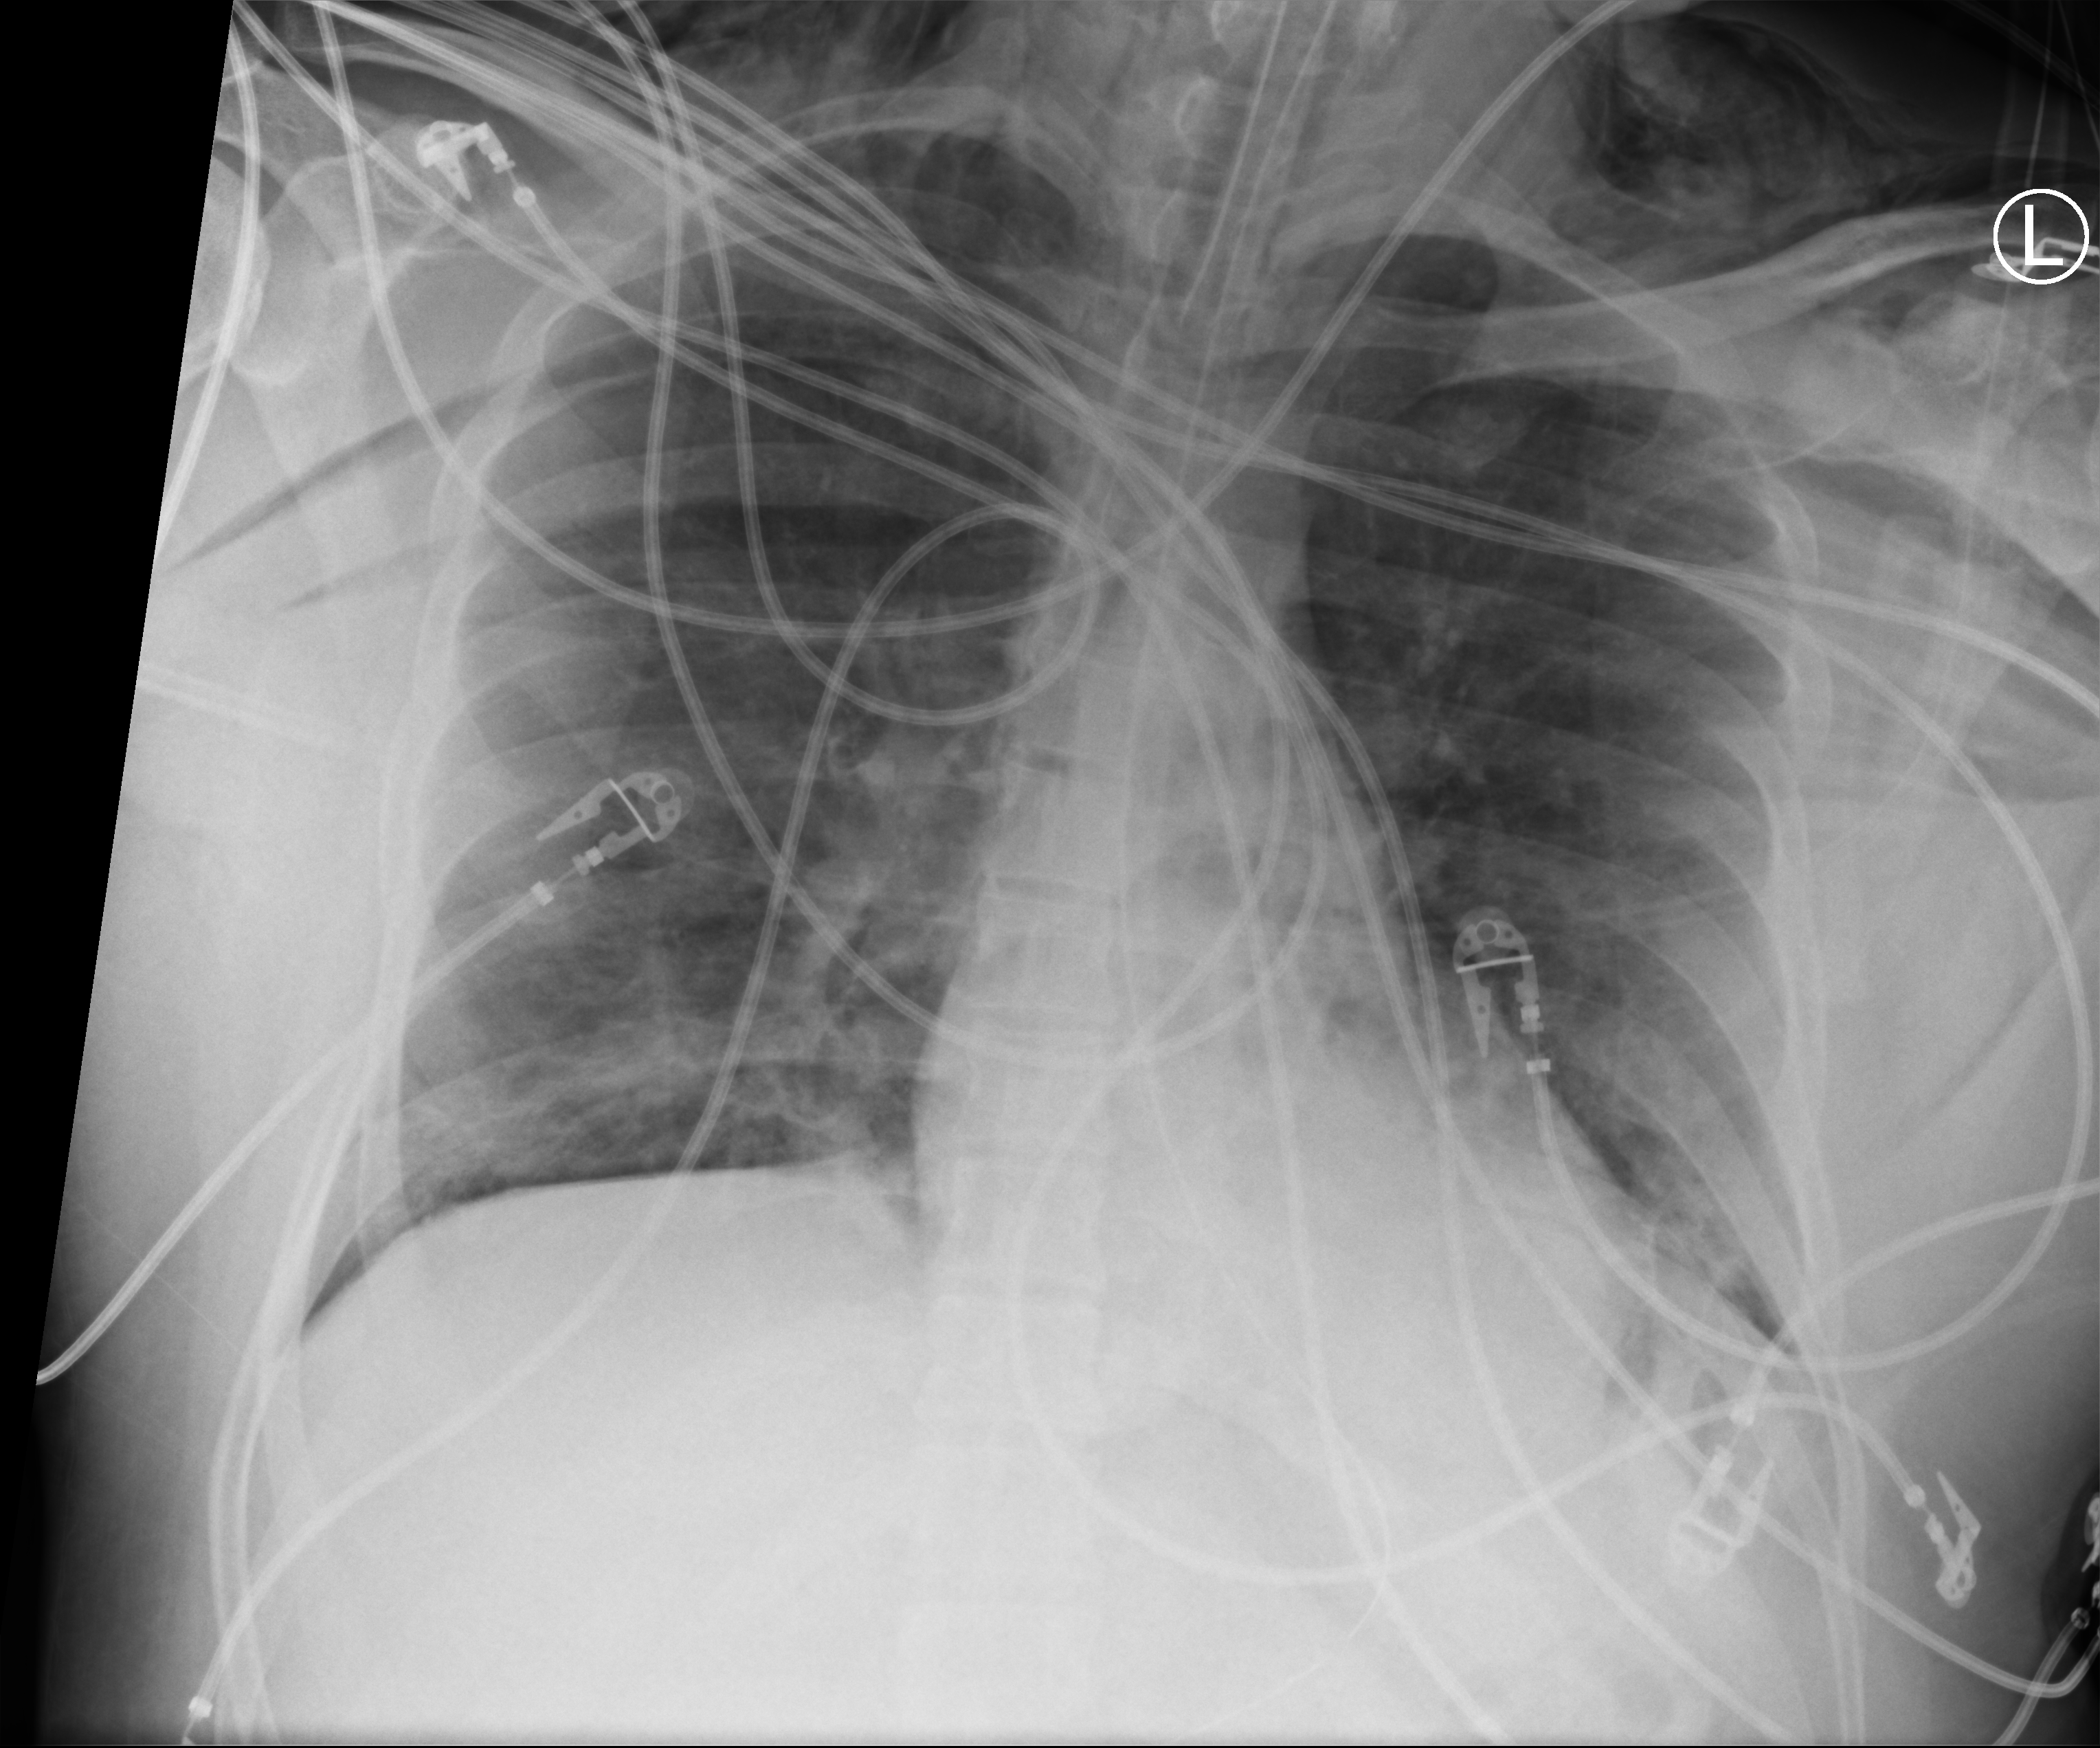
Portable chest radiograph; anteroposterior (AP) projection. Male patient hospitalised with COVID-19, age 18–59 years.
Hospital-stay facts (about this admission, not read from this image; timing relative to this image not recorded): admitted to intensive care during this hospital stay: yes; mechanically ventilated during this hospital stay: yes; chronic kidney disease (admission record): no.